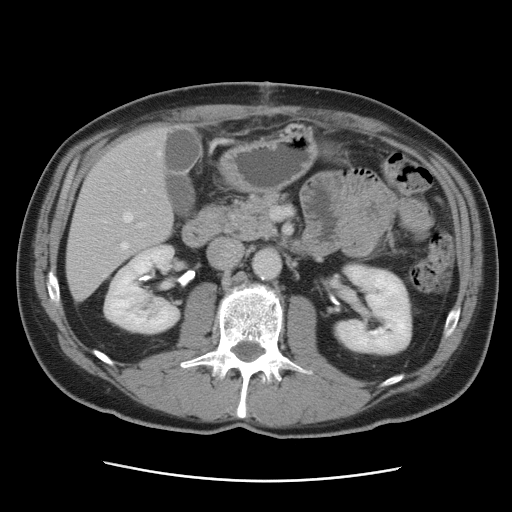
Contrast-enhanced abdominal CT, one axial slice. Slice 38 of 89 in the series (ordered by position). Intravenous contrast given. Soft-tissue window (W 400 / L 40 HU). 5 mm slice thickness. 512 × 512 image matrix, field of view 366 × 366 mm. Male patient, age 59 years. Case-level facts recorded for this patient, not image findings: diagnosis: colorectal cancer liver metastases, imaged before liver resection; multiple liver metastases: yes; largest metastasis: 0.6 cm.
Structures marked on this image (outlined manually by an expert reader):
- hepatic veins: bounding box [x1, y1, x2, y2] px = [104, 143, 162, 276]
- liver: [67, 127, 173, 301]
- planned liver remnant (the part of the liver to remain after resection): [74, 126, 173, 245]
- portal vein (with intrahepatic branches): [138, 190, 146, 227]